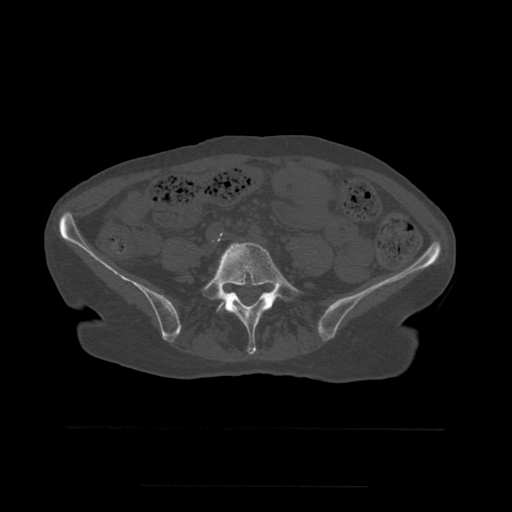
CT including the spine, one axial slice. Position 146 of 544 along the scan axis. Bone window (W 1800 / L 400 HU). 1.25 mm slice thickness. 512 × 512 image matrix, field of view 350 × 350 mm. Patient age 58 years. From the clinical record (not read from this slice): primary cancer: lung.
Structures marked on this image (semi-automatically segmented with operator editing):
- L5 vertebra: bounding box (x1, y1, x2, y2) in pixels: (201, 242, 302, 355)